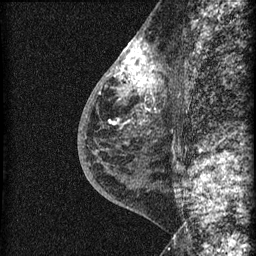
Breast MRI (dynamic contrast-enhanced), one sagittal slice; position 30 of 60 along the scan axis; dynamic contrast-enhanced series, image 2 of 3 at this slice position (ordered by acquisition); 1.5 T; TE 4.2 ms, TR 22.7 ms; 256 × 256 image matrix, field of view 180 × 180 mm. Female patient, age 48 years. From the clinical record (not read from this slice): setting: breast cancer imaged before/during neoadjuvant chemotherapy; receptor status: triple-negative.
Outlined on this slice (semi-automatic segmentation, software-assisted and operator-edited):
- analysis volume of interest (the breast-tissue region the enhancement analysis was run in; not a lesion): bounding box <115,34,169,162> (left, top, right, bottom; pixels)
- tumour enhancement mask (voxels above the 90 % enhancement threshold inside the analysis volume of interest): <115,39,157,91>